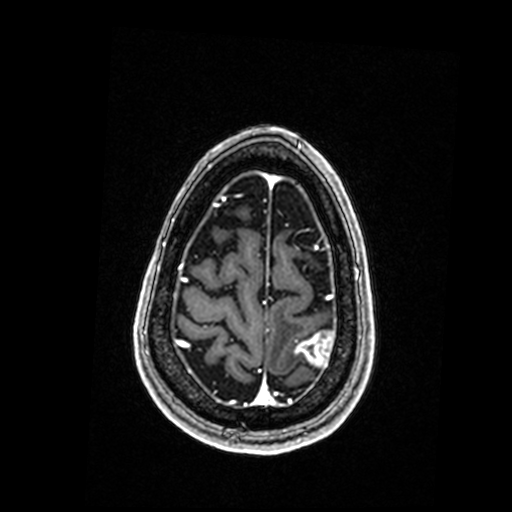
Brain MRI from a brain-tumour surgery series, one axial slice; position 40 of 192 along the scan axis; T1-weighted post-contrast; 0.98 mm slice thickness; 512 × 512 image matrix, field of view 250 × 250 mm. Case-level facts recorded for this patient, not image findings: histopathology: Metastastic Carcinoma, Poorly Differentiated.
Structures marked on this image (expert manual segmentation):
- tumour: bounding box (x1, y1, x2, y2) in pixels: (296, 332, 333, 367)